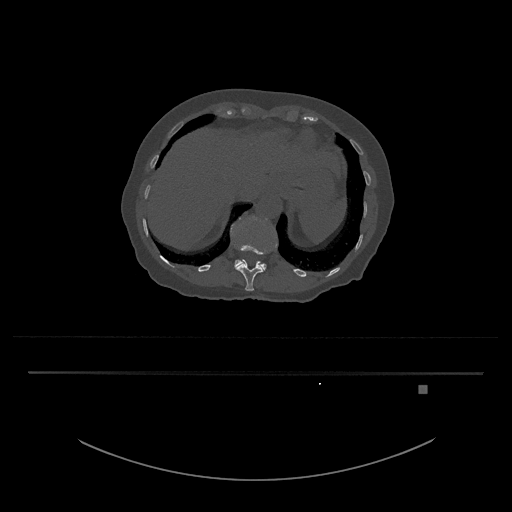
CT including the spine, one axial slice. Position 593 of 797 along the scan axis. 120 kVp. Bone window (W 1800 / L 400 HU). 512 × 512 image matrix. Female patient, age 57 years. From the clinical record (not read from this slice): primary cancer: cervical.
Structures marked on this image (semi-automatically segmented with operator editing):
- L1 vertebra: bounding box <233,218,268,271> (left, top, right, bottom; pixels)
- T12 vertebra: <233,235,266,291>